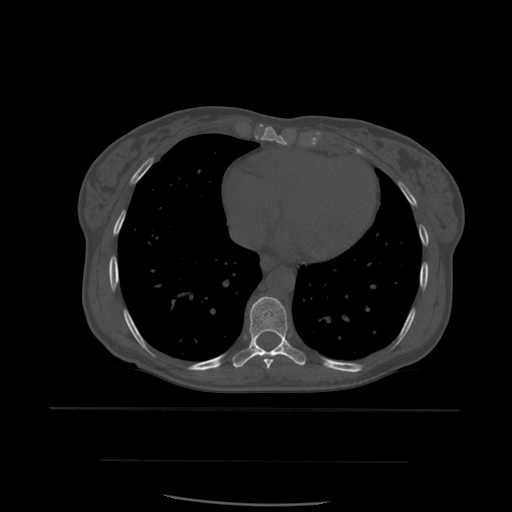
CT including the spine, one axial slice. Slice 340 of 574 in the series (ordered by position). Bone window (W 1800 / L 400 HU). 512 × 512 image matrix, field of view 392 × 392 mm. Patient age 48 years. From the clinical record (not read from this slice): primary cancer: lung.
Annotated regions visible in this slice (semi-automatic segmentation, software-assisted and operator-edited):
- T8 vertebra: bounding box [x1, y1, x2, y2] px = [264, 356, 274, 370]
- T9 vertebra: [233, 297, 306, 368]